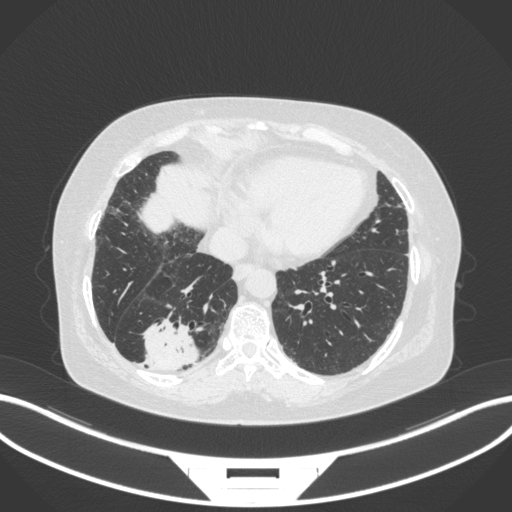
Chest CT, one axial slice; position 64 of 303 along the scan axis; lung window (W 1500 / L -600 HU); 1 mm slice thickness; 512 × 512 image matrix. Patient: female, 65 years. From the clinical record (not read from this slice): clinical TNM (as recorded): T2b N1 M0; histopathological grade: G1.
Structures marked on this image (rectangle marked by the reading radiologist):
- lung tumour (recorded histology: adenocarcinoma): bounding box [x1, y1, x2, y2] px = [139, 319, 203, 373]